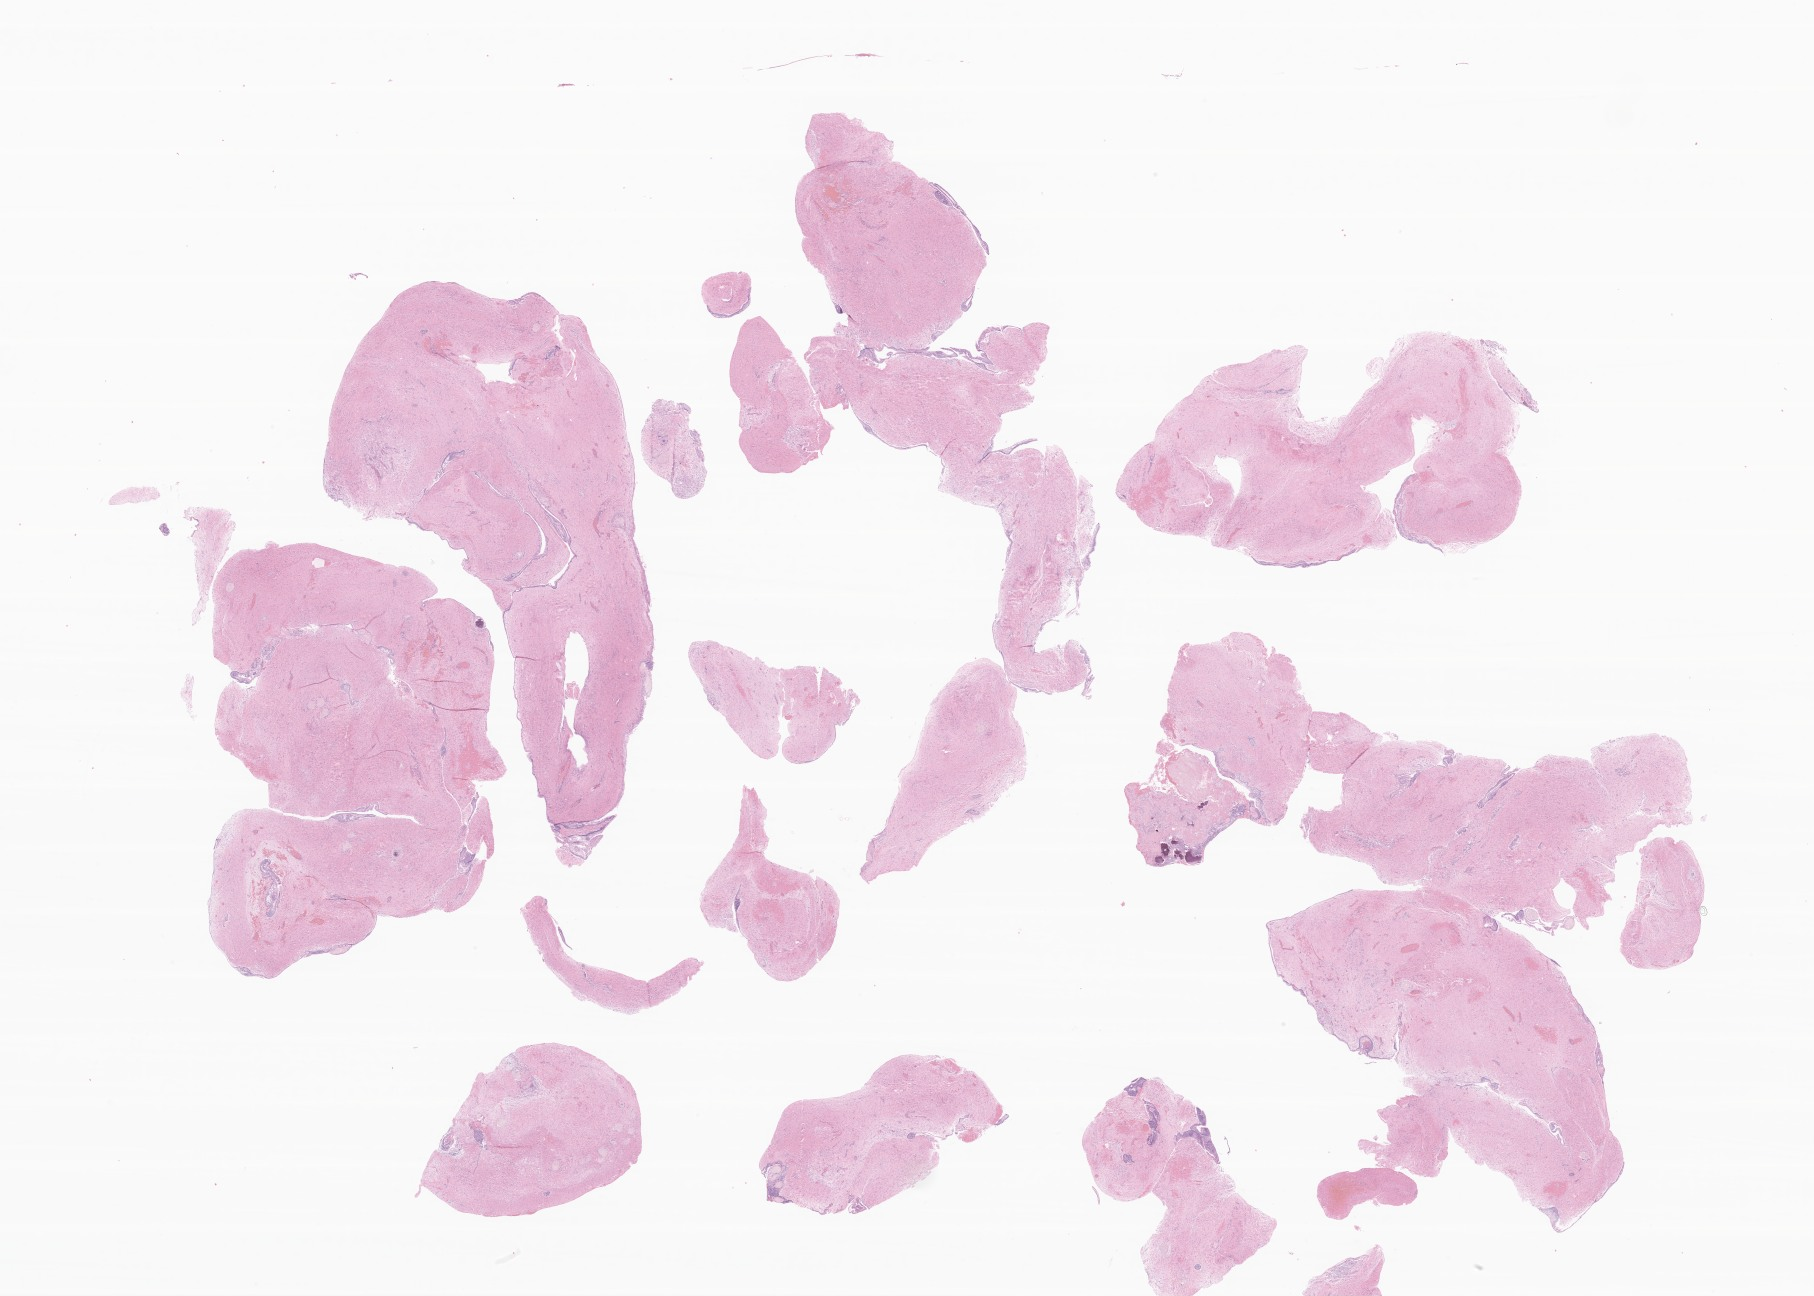
Digitized hematoxylin and eosin (H&E)-stained section of tumor tissue from the craniopharyngeal duct, low-resolution overview of the scanned area, about 30.6 x 21.9 mm. Formalin-fixed, paraffin-embedded (FFPE) tissue. Patient male; age 161 months (13 years 5 months).
* recorded diagnosis: Craniopharyngioma, adamantinomatous